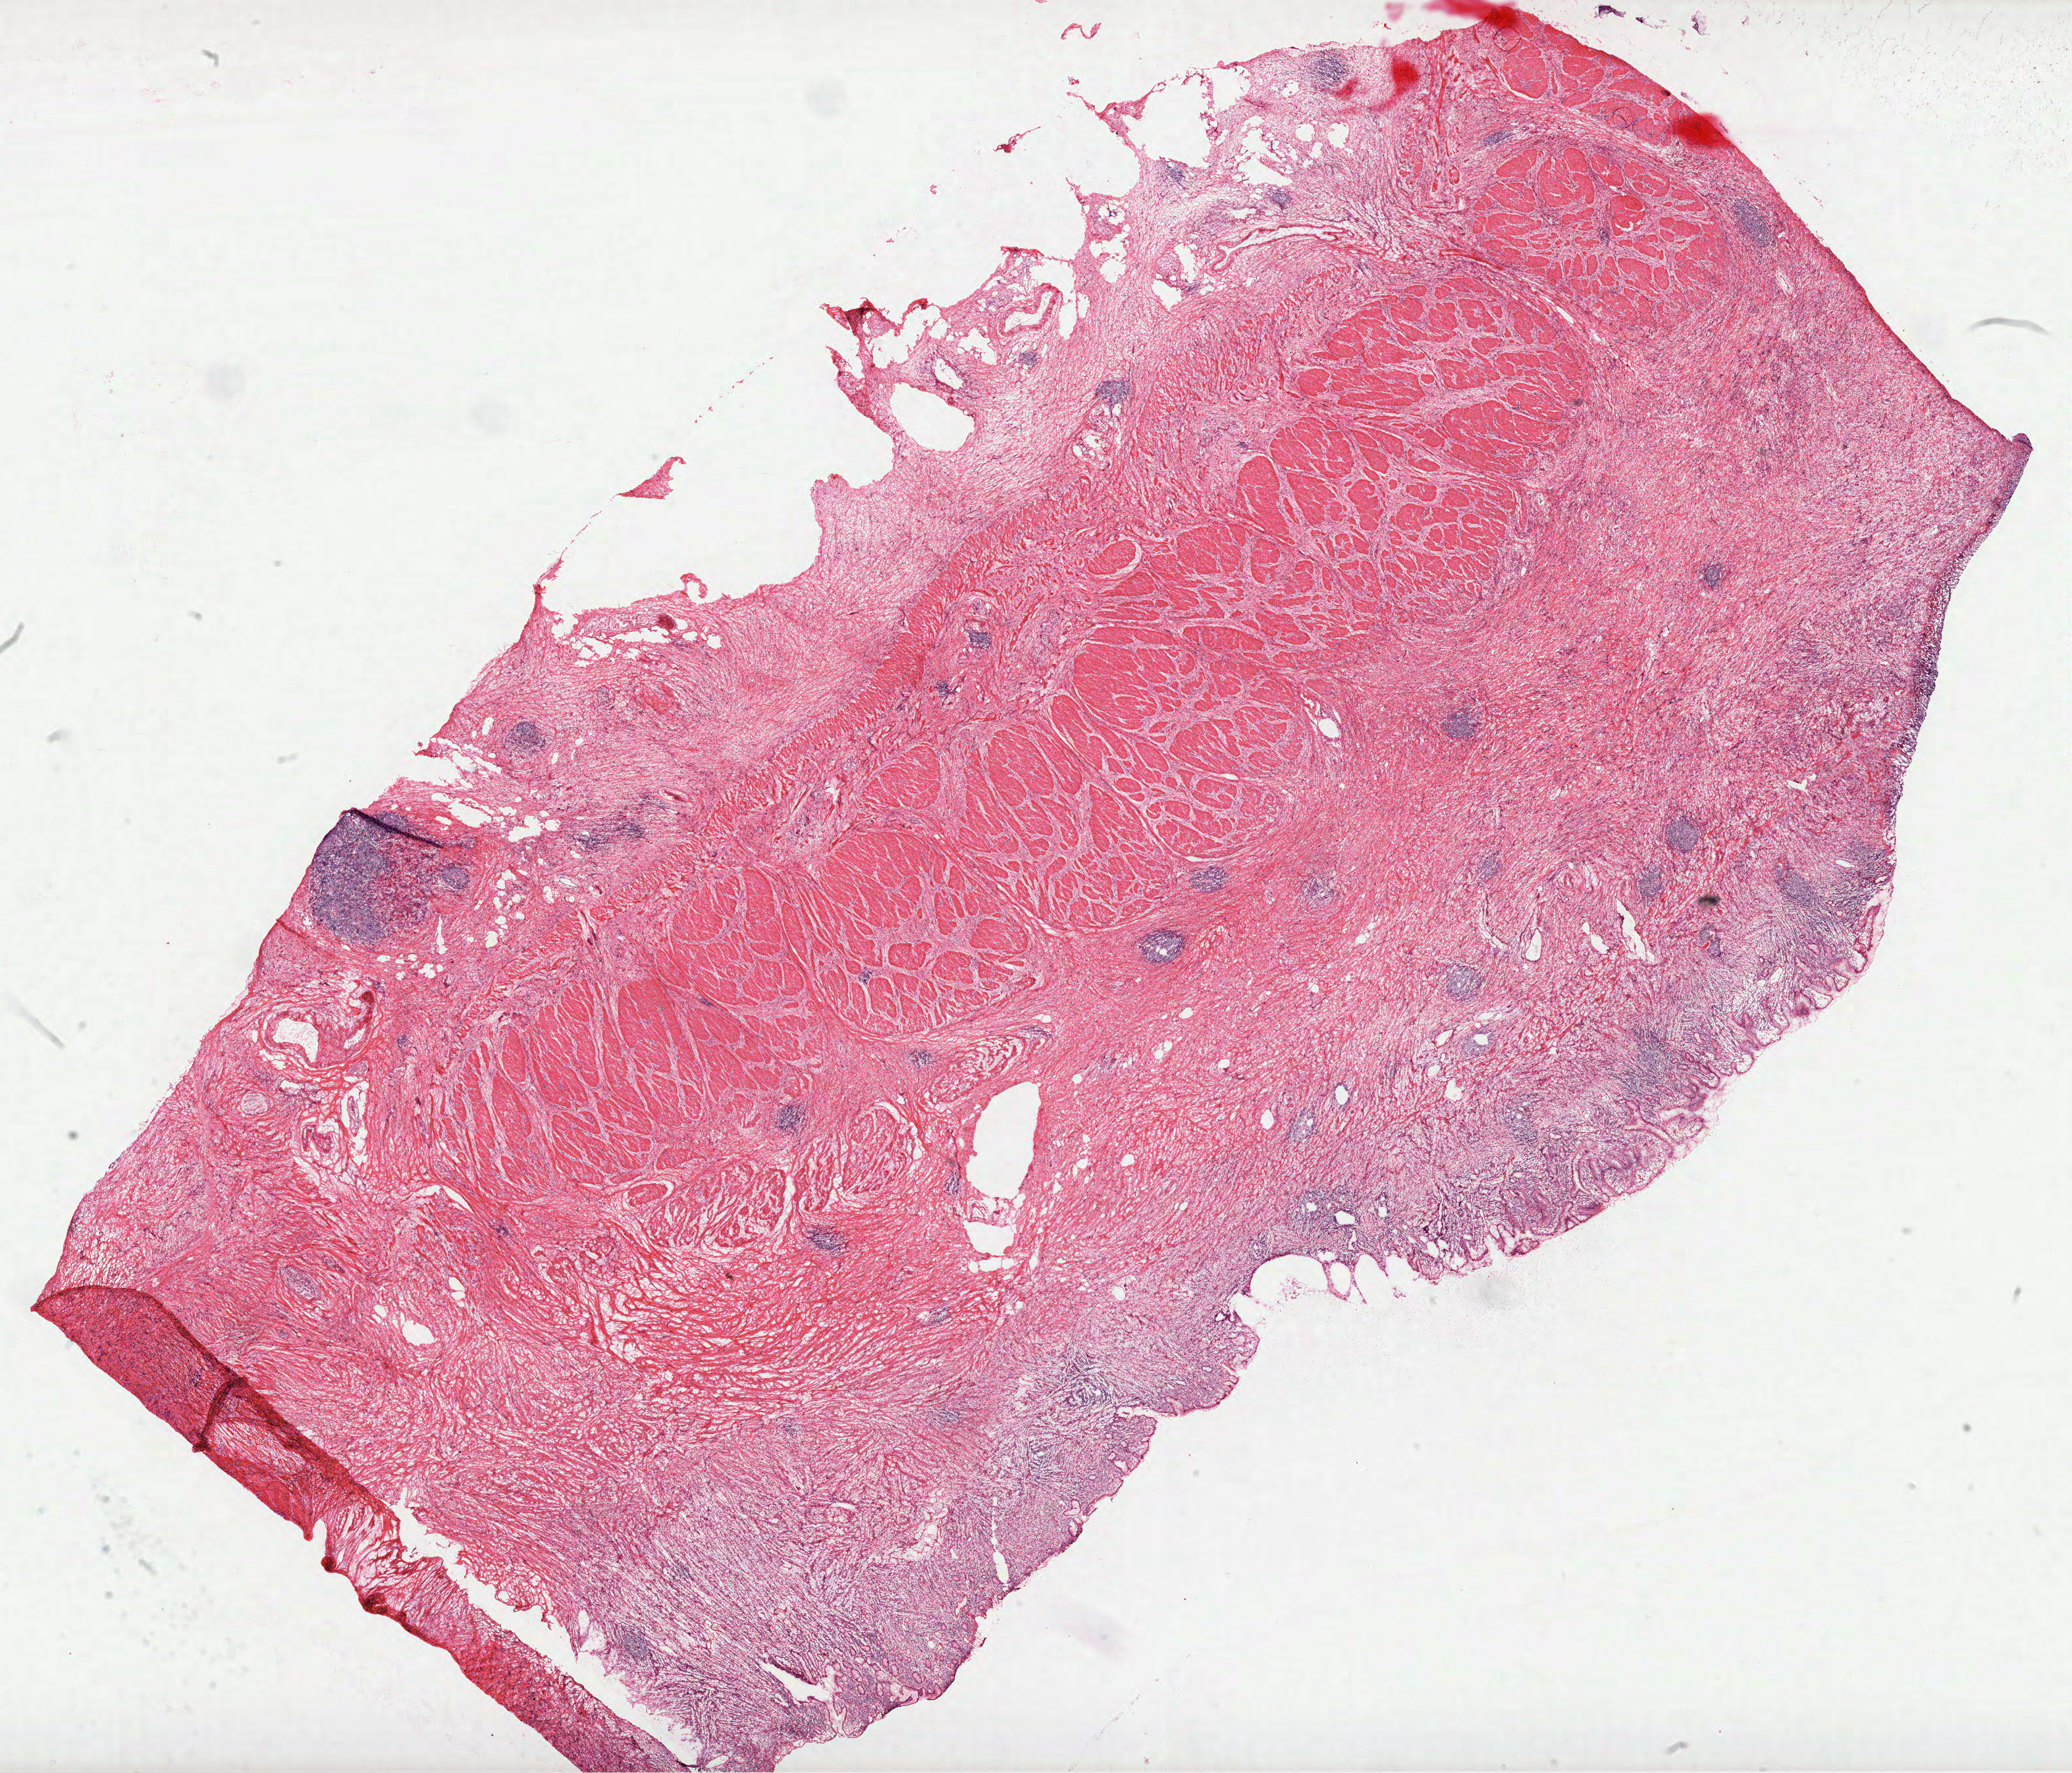
Digitized H&E tissue section (whole slide) — a low-resolution overview of the entire scanned area, about 25.4 x 21.7 mm (slide scanned at 40x); frozen section; sample: primary tumour, stomach. Female patient; age at initial diagnosis 63 years. Histologic grade: G3 (poorly differentiated). Pathologist review of this section (percent, as recorded): tumour cells 52%, tumour nuclei 60%, normal cells 8%, stromal cells 40%, necrosis 0%.
Lymph nodes positive (case pathology): 1 of 3 examined. AJCC pathologic stage: IIIB. Pathologic diagnosis: Carcinoma, diffuse type (fundus of stomach).